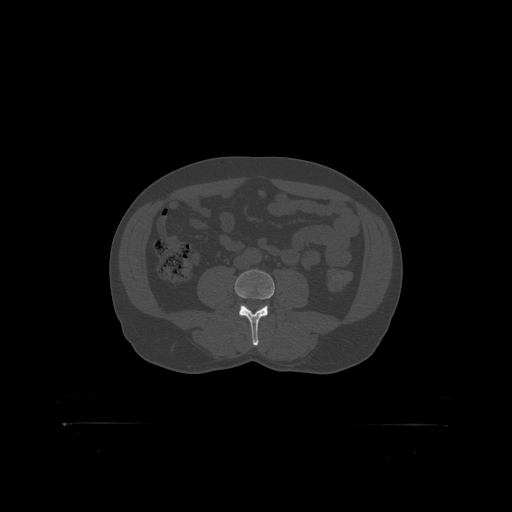
CT including the spine, one axial slice; slice 232 of 399 in the series (ordered by position); 120 kVp; bone window (W 1800 / L 400 HU); 512 × 512 image matrix, field of view 650 × 650 mm. Patient: male, 46 years. Case-level facts recorded for this patient, not image findings: primary cancer: skin.
Outlined on this slice (semi-automatic segmentation, software-assisted and operator-edited):
- L4 vertebra: box from (x=235, y=270) to (x=275, y=319) px